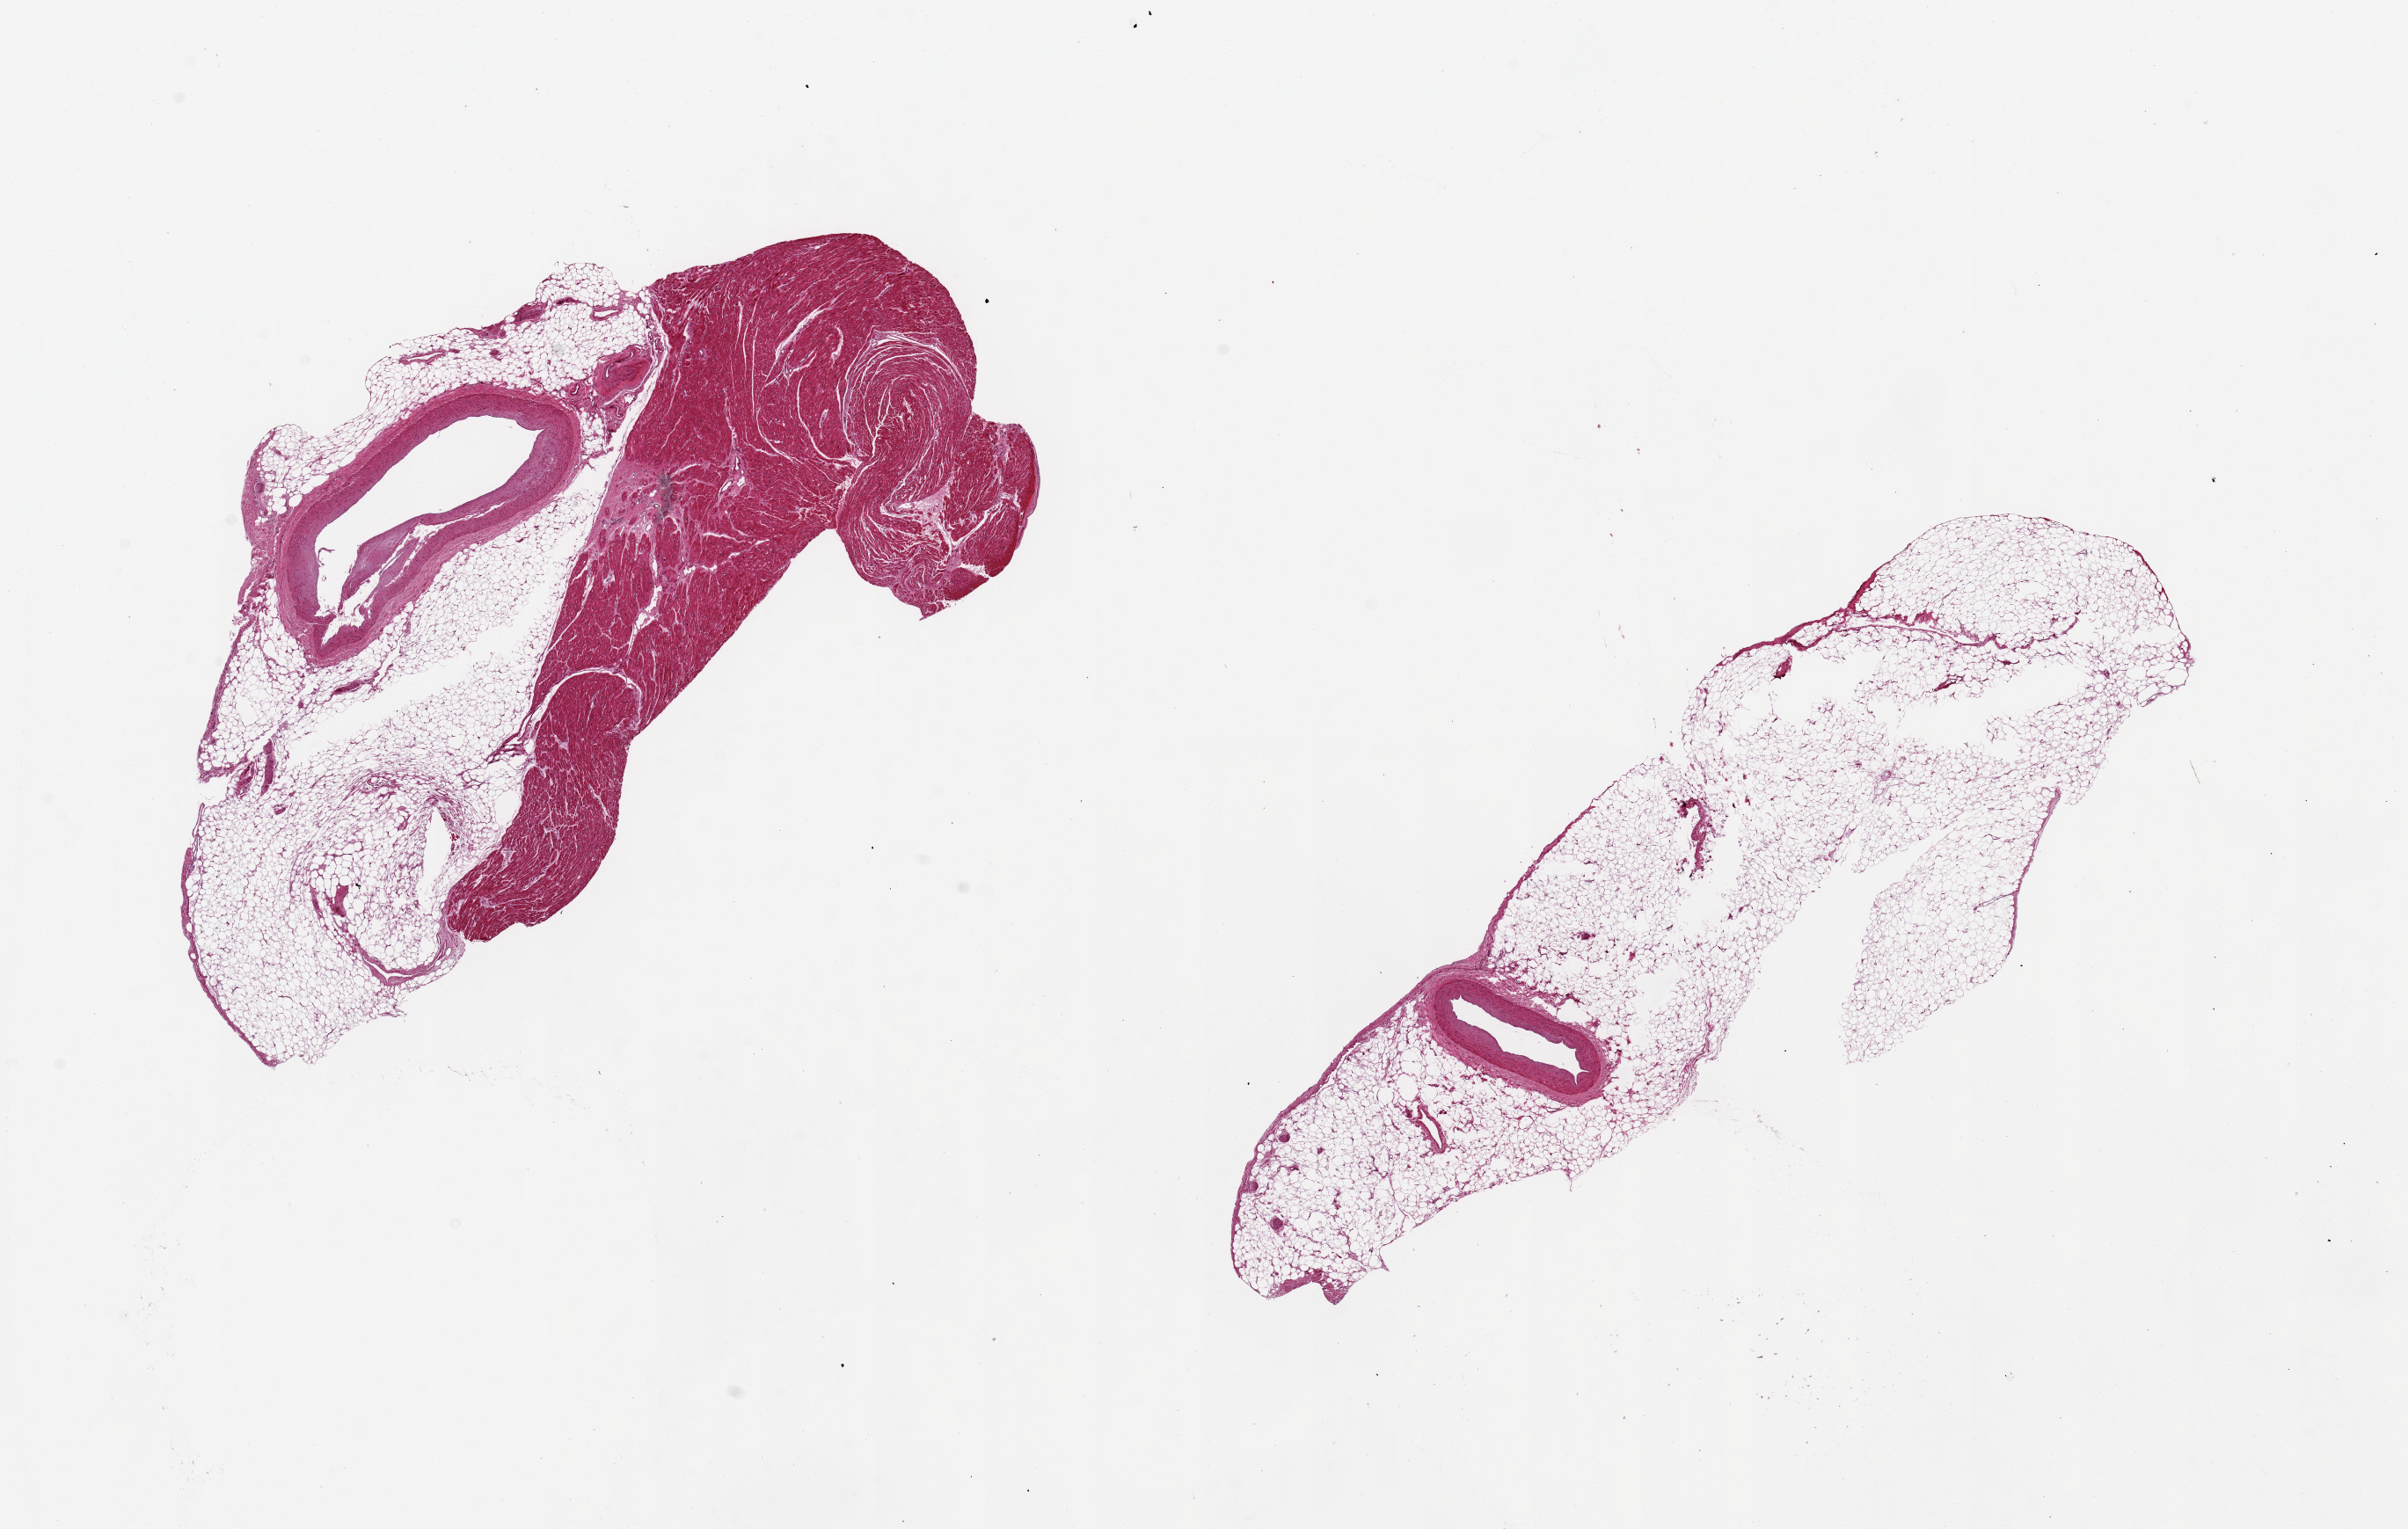
Hematoxylin and eosin (H&E) whole-slide image, brightfield, shown as a low-resolution overview of the whole scanned area (about 21.7 x 13.8 mm, slide scanned at 20x). PAXgene-fixed, paraffin-embedded tissue. Sampled site (target tissue): coronary artery. Tissue donor sample. Donor: female.
Reviewer comment on this tissue sample: 2 pieces, 9x6 & 10x4mm; 1 piece is 90% external adipose, other is 60% adipose and myocardium.